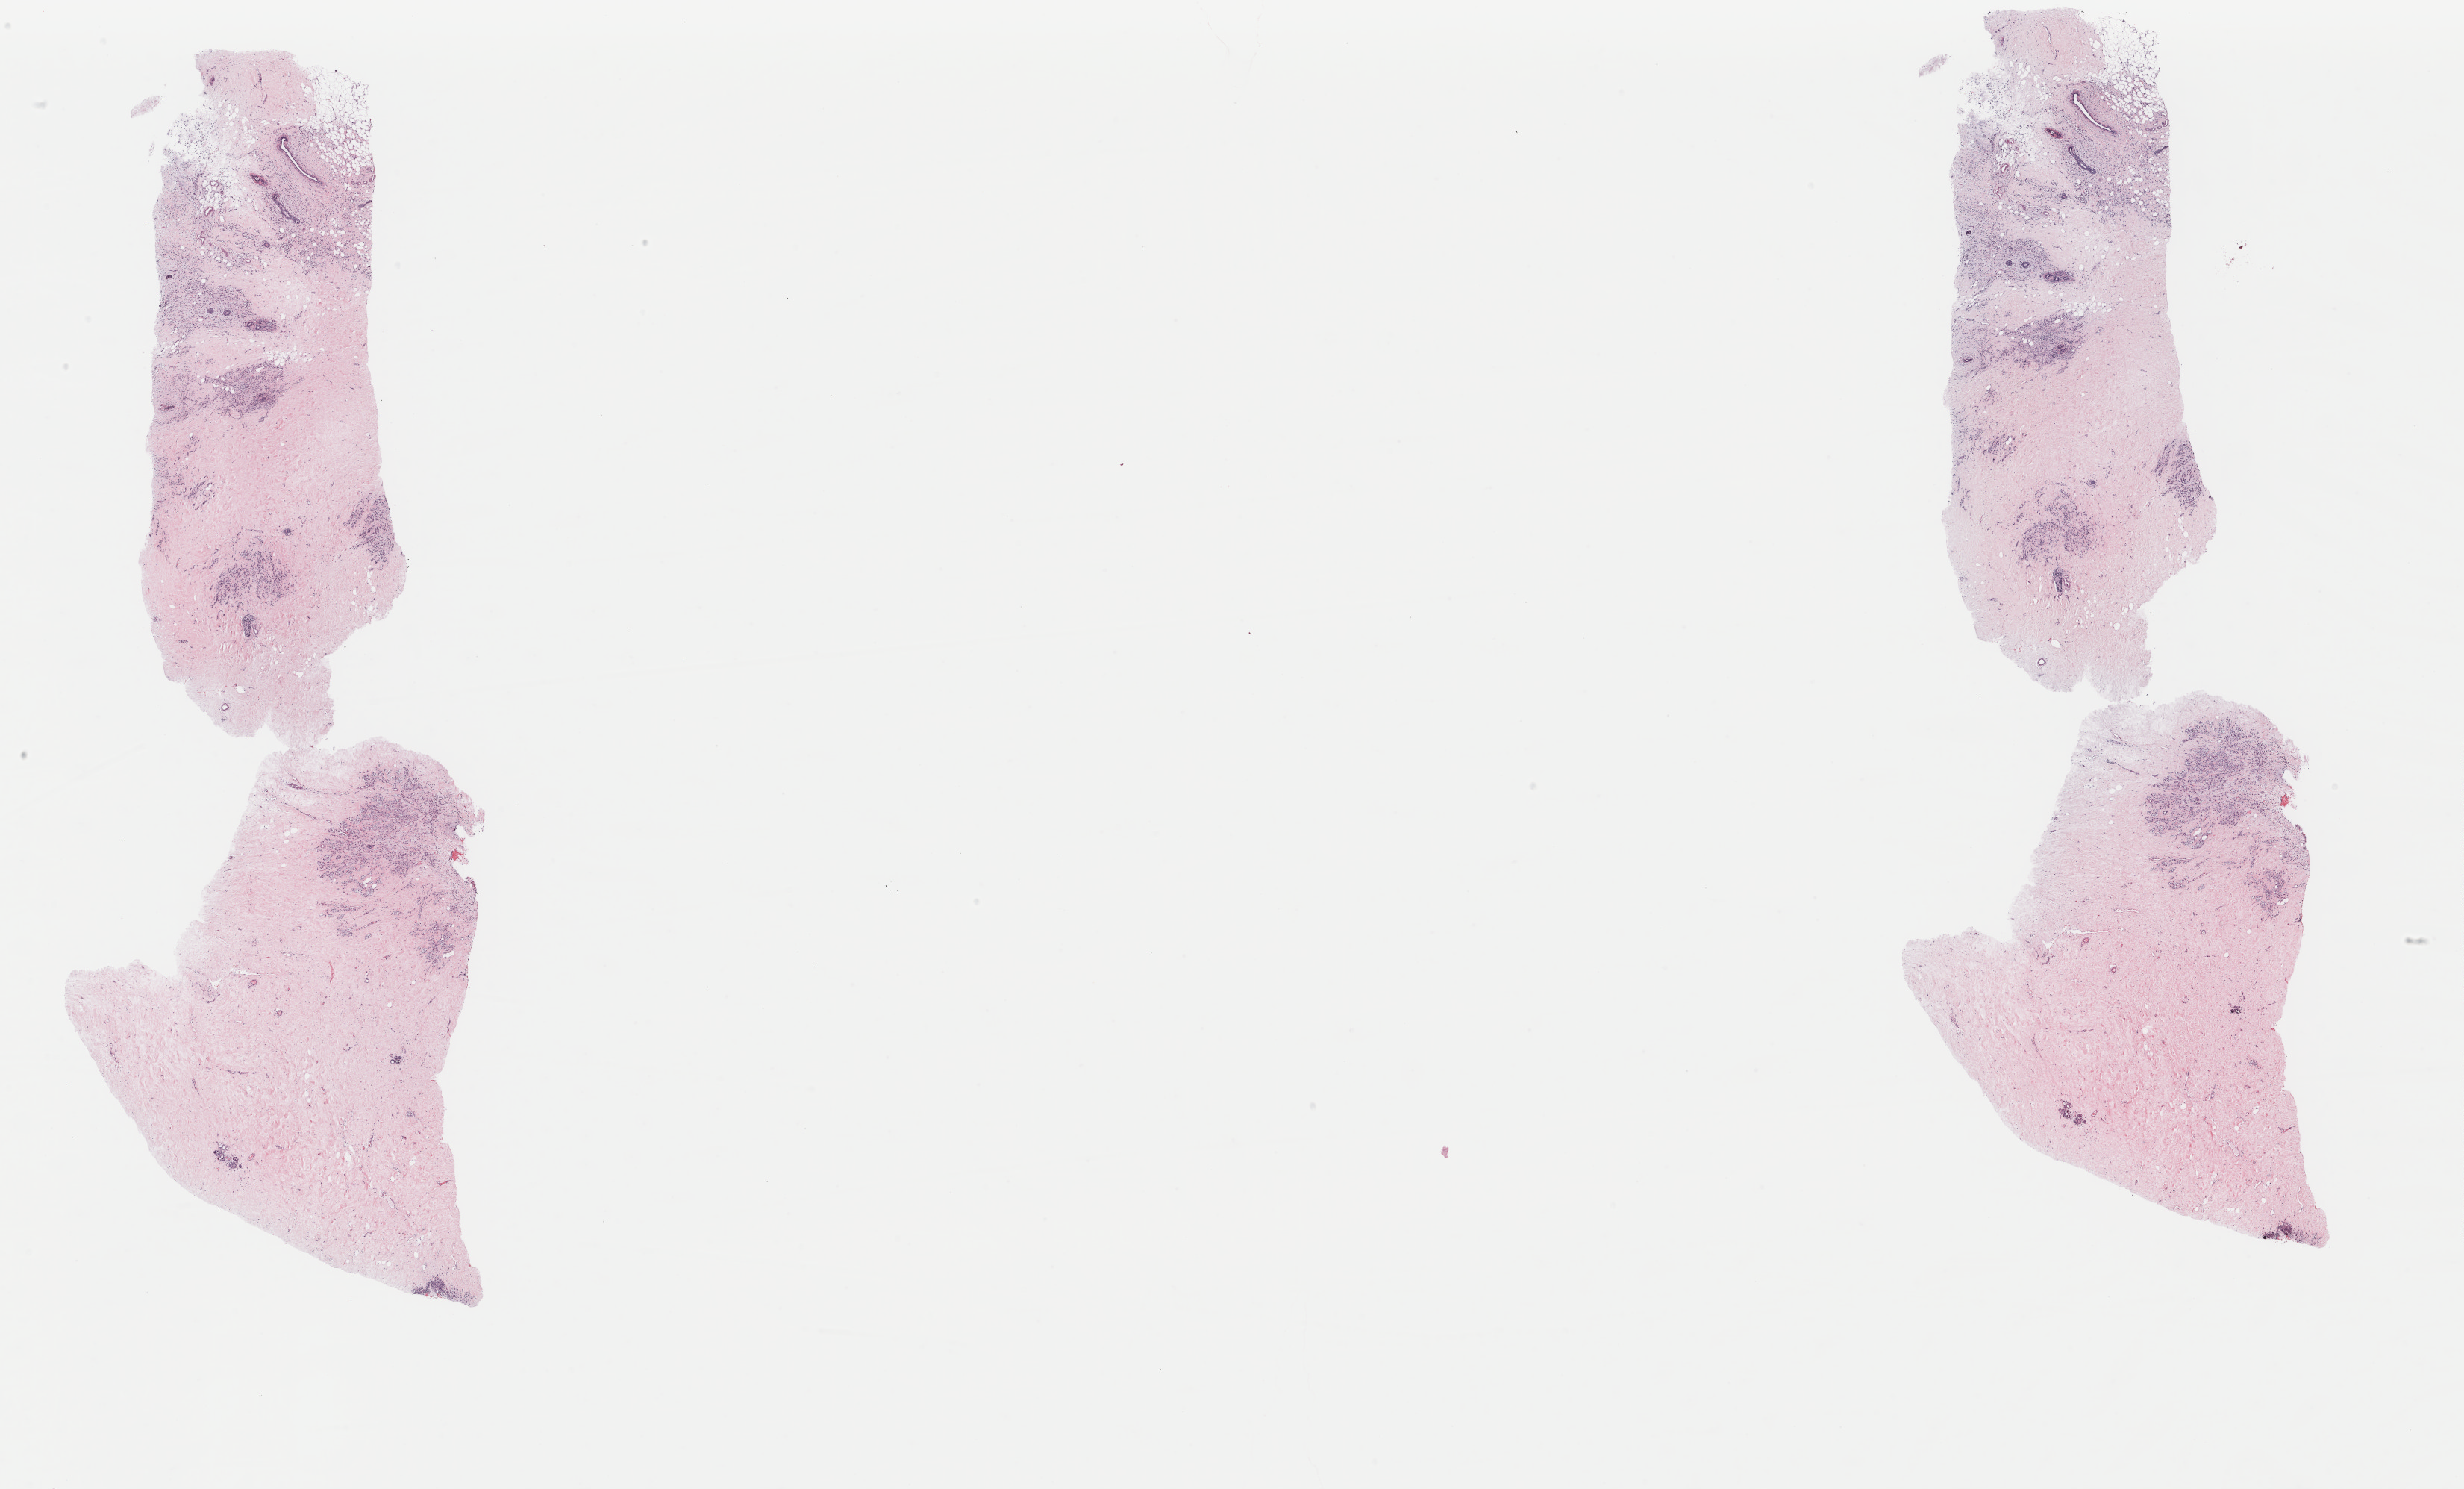
Whole-slide histology image, H&E-stained, shown as a low-resolution overview of the whole scanned area (about 26.2 x 15.8 mm, acquisition: 40x scan); FFPE section; primary tumour sample from the breast. Female, age 62 years at initial diagnosis.
Diagnosis: Lobular carcinoma, NOS. Lymph nodes positive (case pathology): 0 of 1 examined. Laterality: right. AJCC pathologic stage: IIB.